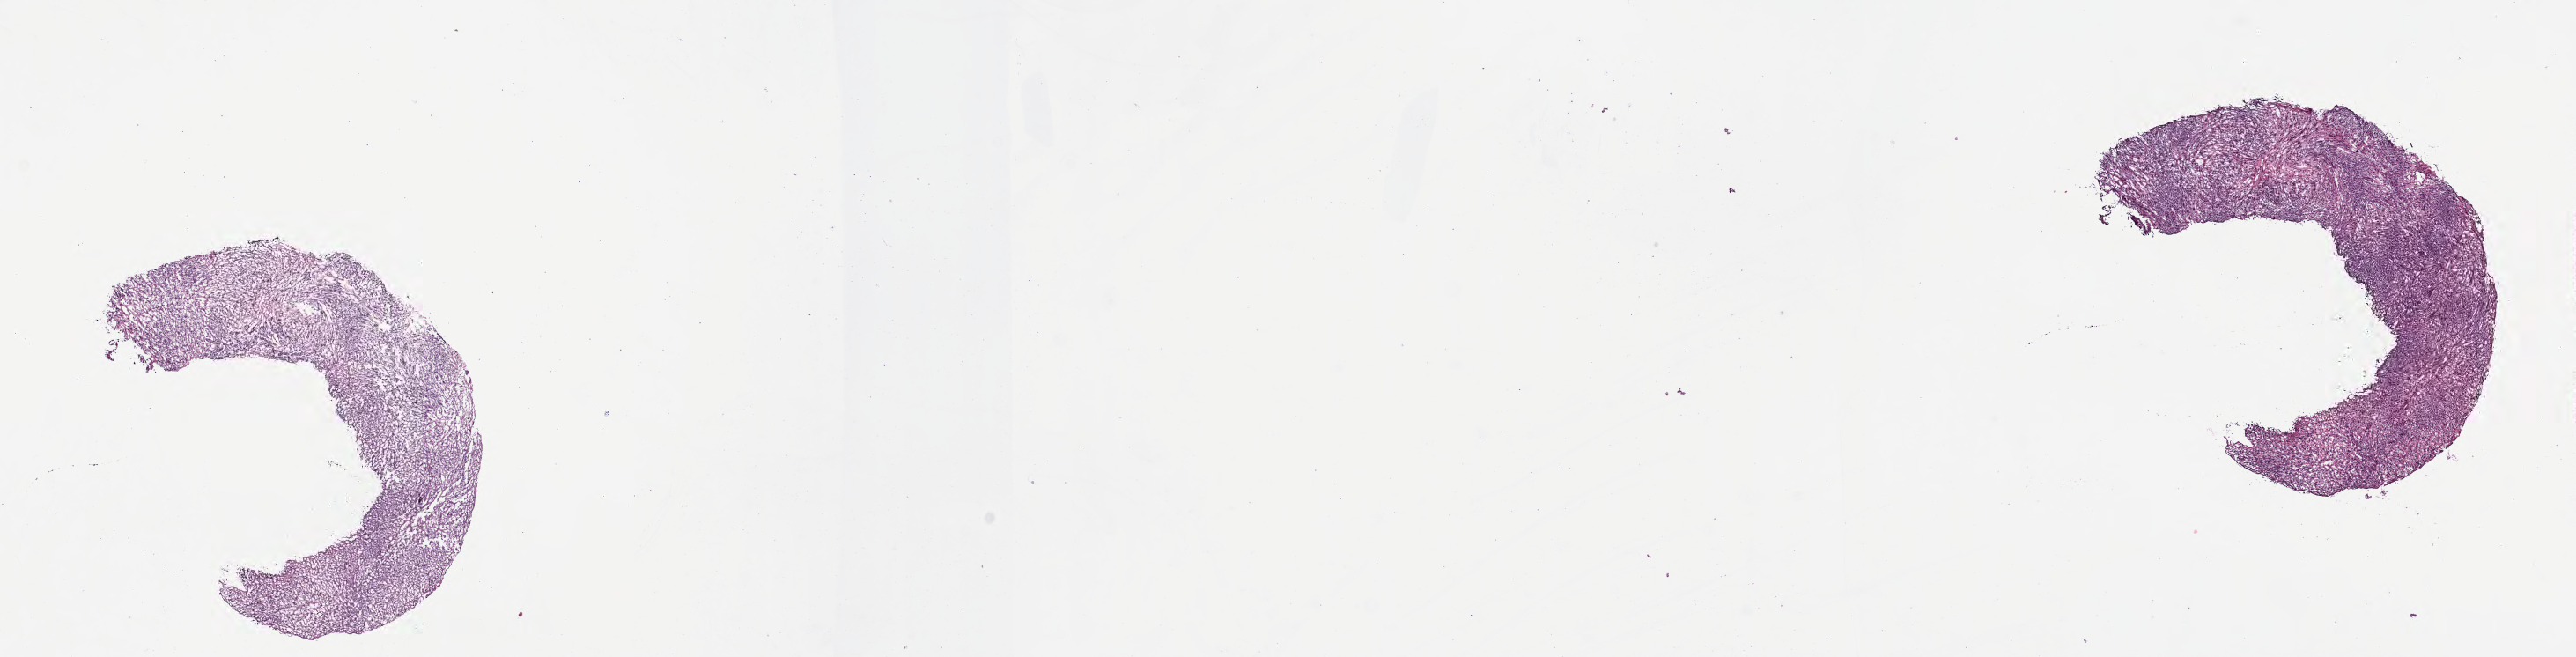
Digitized hematoxylin and eosin (H&E)-stained section of tumor tissue from the soft tissues of head and neck — whole scanned area (about 23.6 x 6.0 mm) shown as a low-resolution overview, frozen section. Patient female; age 73 months (6 years 1 month).
- diagnosis (ICD-O-3 morphology term): Rhabdomyosarcoma, NOS